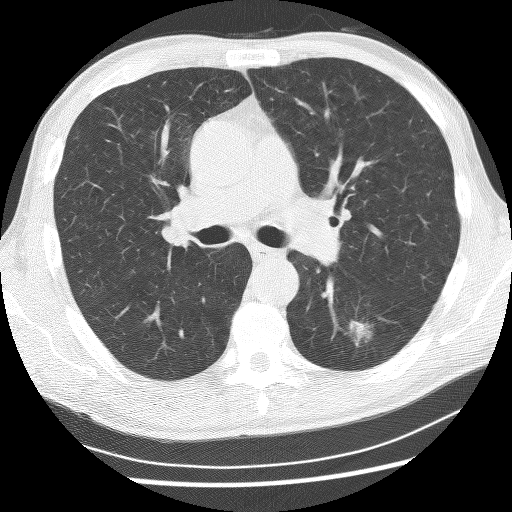
Low-dose screening chest CT, one axial slice; slice 152 of 253 in the series (ordered by position); reconstruction kernel BONE; 120 kVp; lung window (W 1500 / L -600 HU); 2.5 mm slice thickness; 512 × 512 image matrix.
Structures marked on this image (manually delineated by an expert):
- lesion 1 (tumor, lower lobe of left lung): bounding box (x1, y1, x2, y2) in pixels: (349, 321, 372, 344)